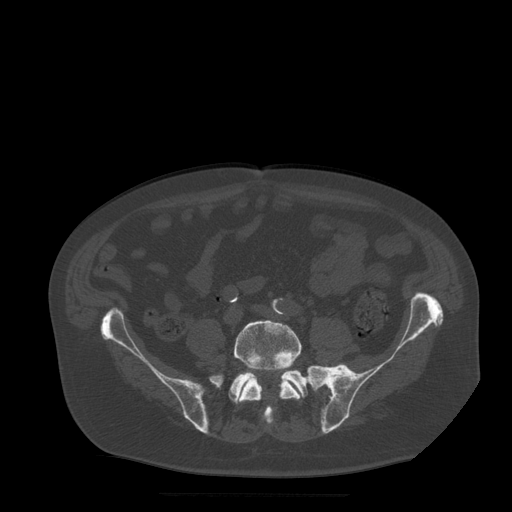
CT including the spine, one axial slice; slice 82 of 522 in the series (ordered by position); bone window (W 1800 / L 400 HU); 1.25 mm slice thickness; 512 × 512 image matrix. Patient age 72 years. From the clinical record (not read from this slice): primary cancer: prostate.
Outlined on this slice (semi-automatically segmented with operator editing):
- L5 vertebra: bounding box (x1, y1, x2, y2) in pixels: (234, 320, 302, 423)